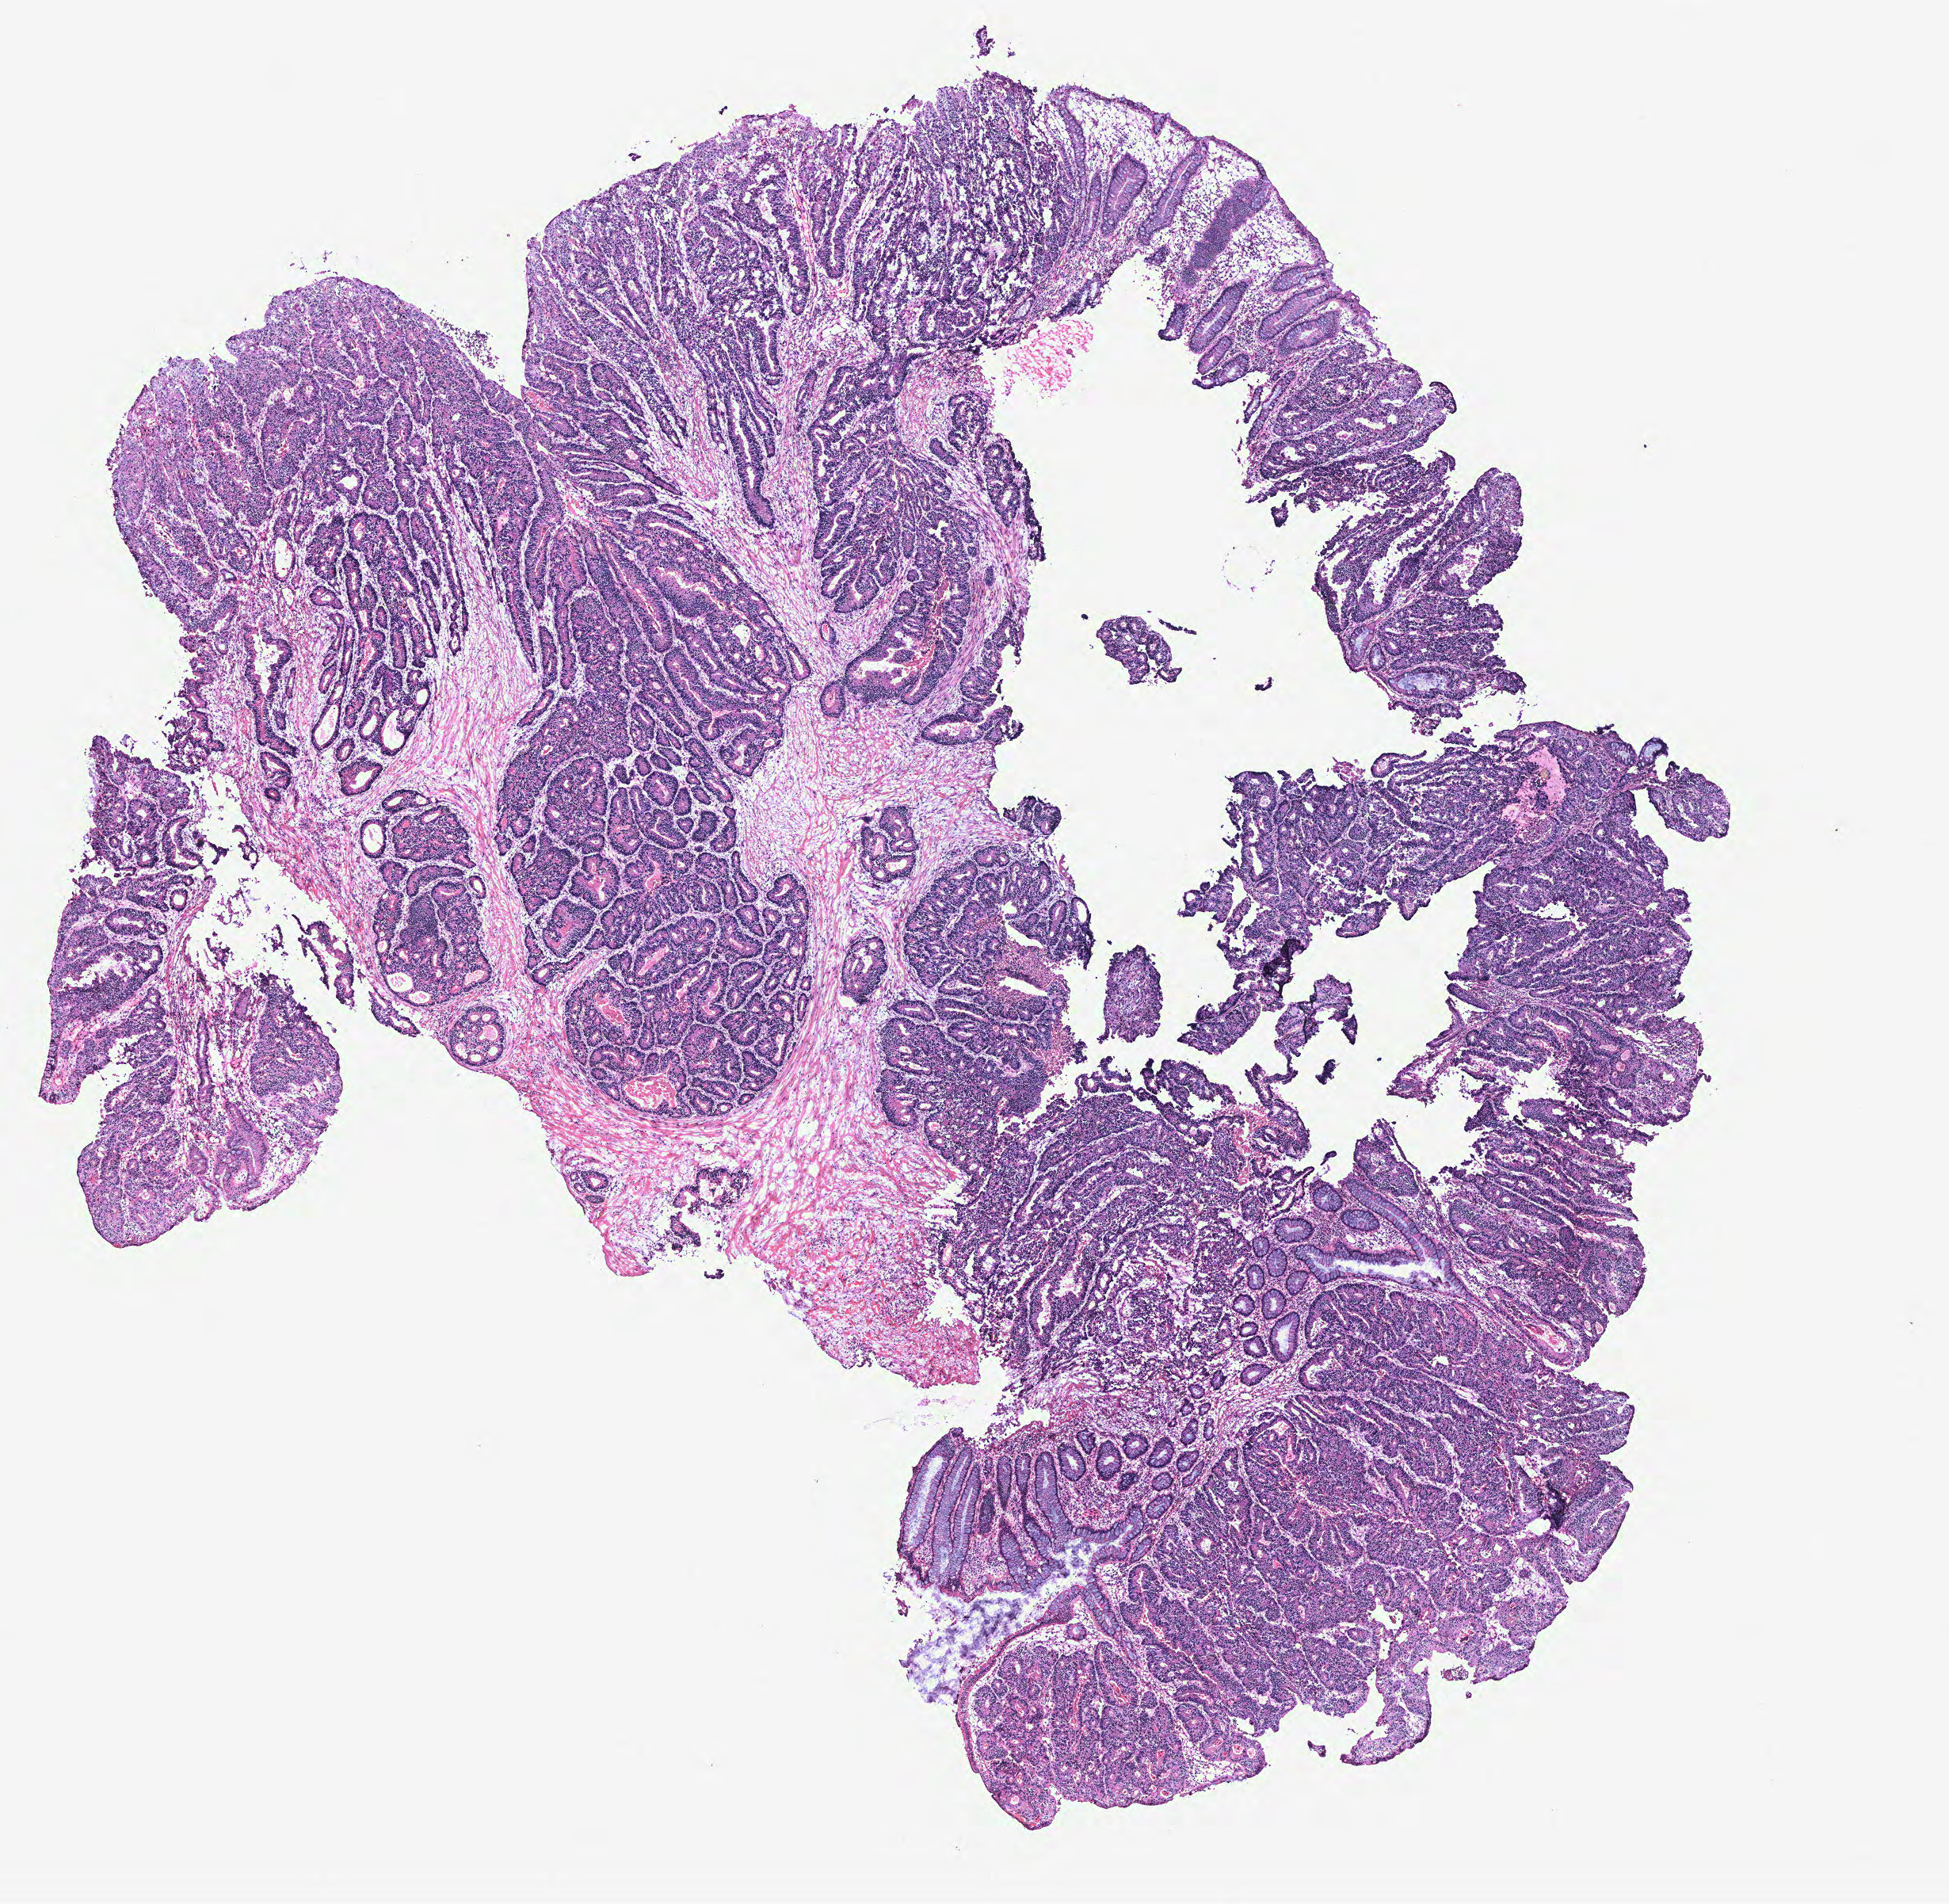
Whole-slide histology image, Hematoxylin and eosin (H&E) stained, shown as a low-resolution overview of the whole scanned area (about 9.8 x 9.6 mm, acquisition: 40x scan). Colon, tissue type not recorded.
Patient diagnosis (cohort enrolment): colon cancer (colon).